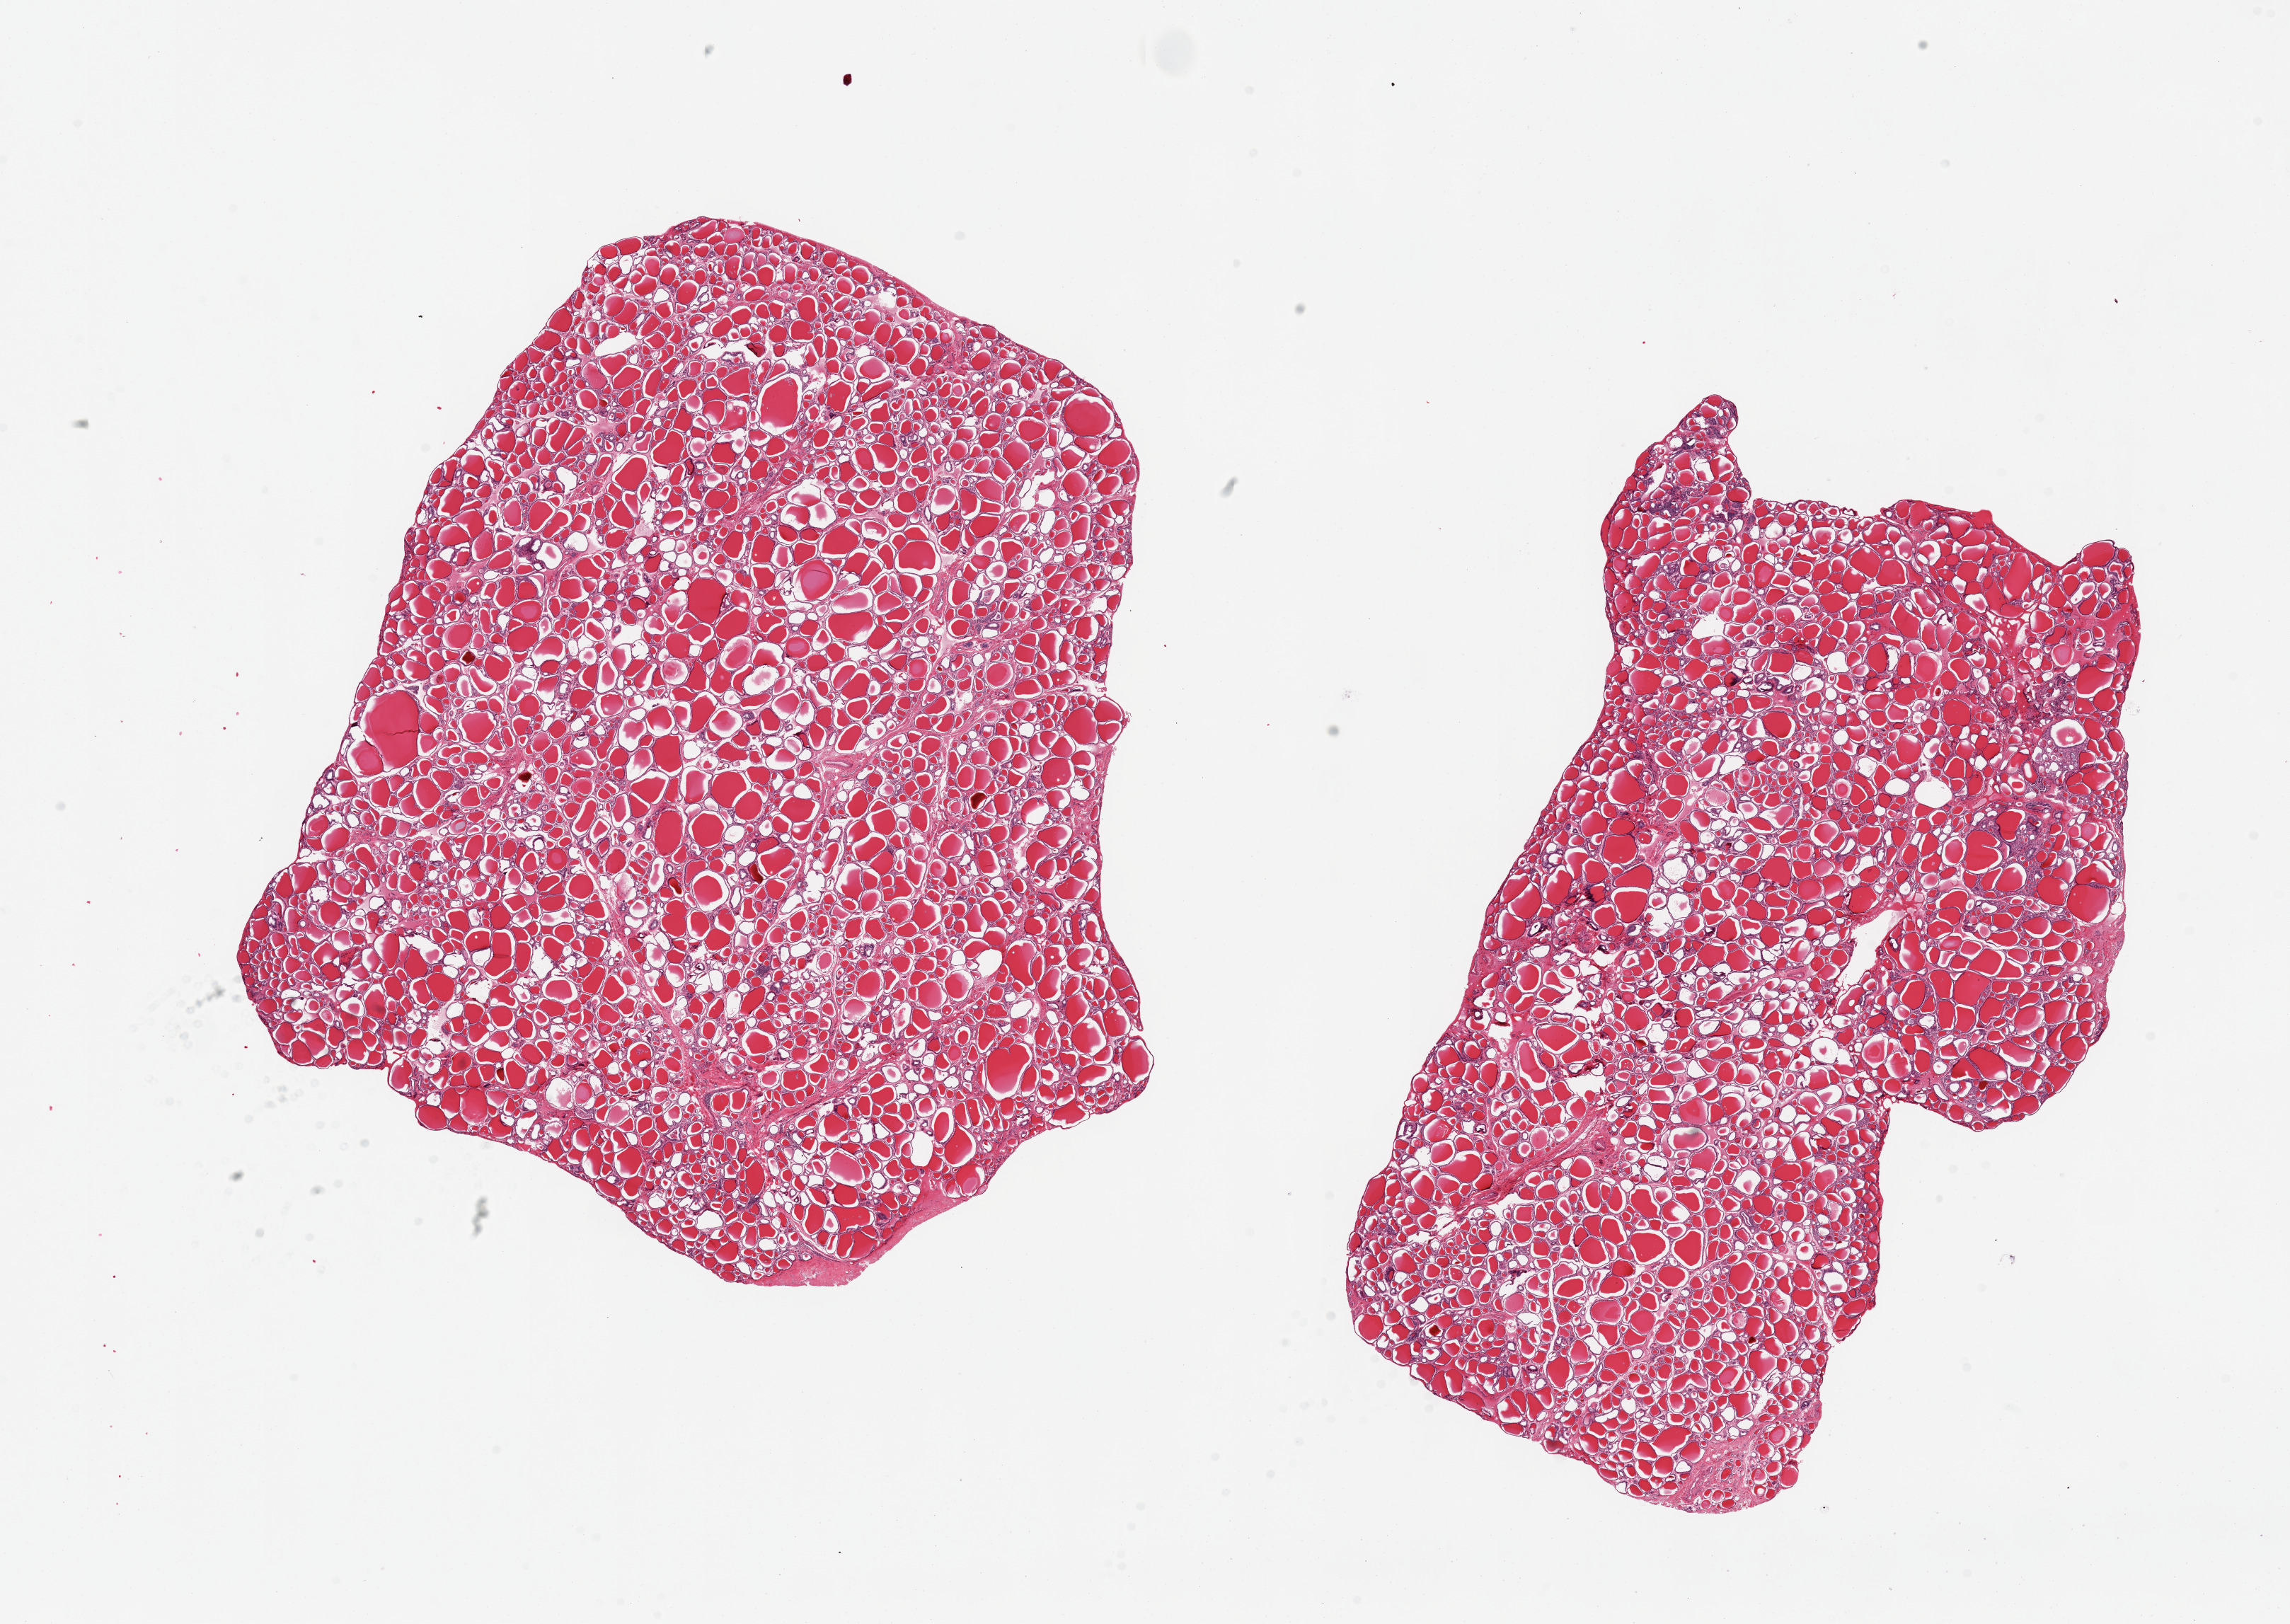
Digitized hematoxylin and eosin (H&E)-stained section, a low-resolution overview of the entire scanned area, about 25.6 x 18.2 mm (slide scanned at 20x), PAXgene-fixed paraffin-embedded (PFPE) section, target tissue: thyroid, donor tissue sample. Male donor.
Pathologist's review note for this sample: 2 pieces, 11x10 and 11x6.5mm; well sampled.